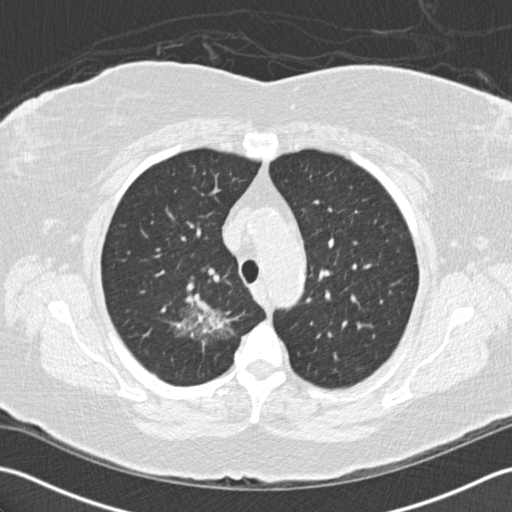
Axial slice from a low-dose chest CT screening exam; first (baseline) screen; lung window (W 1500 / L -600 HU); 2 mm slice thickness; slice 34 of 156 in the series. Female participant, aged 72 years at enrolment.
Lesion marked by an expert reader, box from (x=139, y=274) to (x=238, y=369) px. The screening reader recorded 2 non-calcified nodules or masses ≥4 mm on this exam (right lower lobe, right lower lobe); which of them this box marks is not recorded. Official screen result: positive, change unspecified: nodule(s) >= 4 mm or enlarging nodule(s), mass(es), or other non-specific abnormalities suspicious for lung cancer. Participant outcome: lung cancer diagnosed 494 days after this screen — bronchiolo-alveolar adenocarcinoma, NOS, right upper lobe, stage IIIB (AJCC 6th edition), 45 mm at pathology.